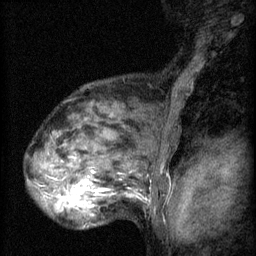
Breast MRI (dynamic contrast-enhanced), one sagittal slice. Slice 45 of 60 in the series (ordered by position). 3 images stored at this slice position (order not interpretable as contrast timing). 1.5 T. TE 4.2 ms, TR 8.2 ms. 2 mm slice thickness. 256 × 256 image matrix, field of view 180 × 180 mm. Female patient, age 48 years.
Structures marked on this image (semi-automatically segmented with operator editing):
- analysis volume of interest (the breast-tissue region the enhancement analysis was run in; not a lesion): bounding box [x1, y1, x2, y2] px = [48, 160, 125, 217]
- tumour enhancement mask (voxels above the 70 % enhancement threshold inside the analysis volume of interest): [54, 182, 94, 213]